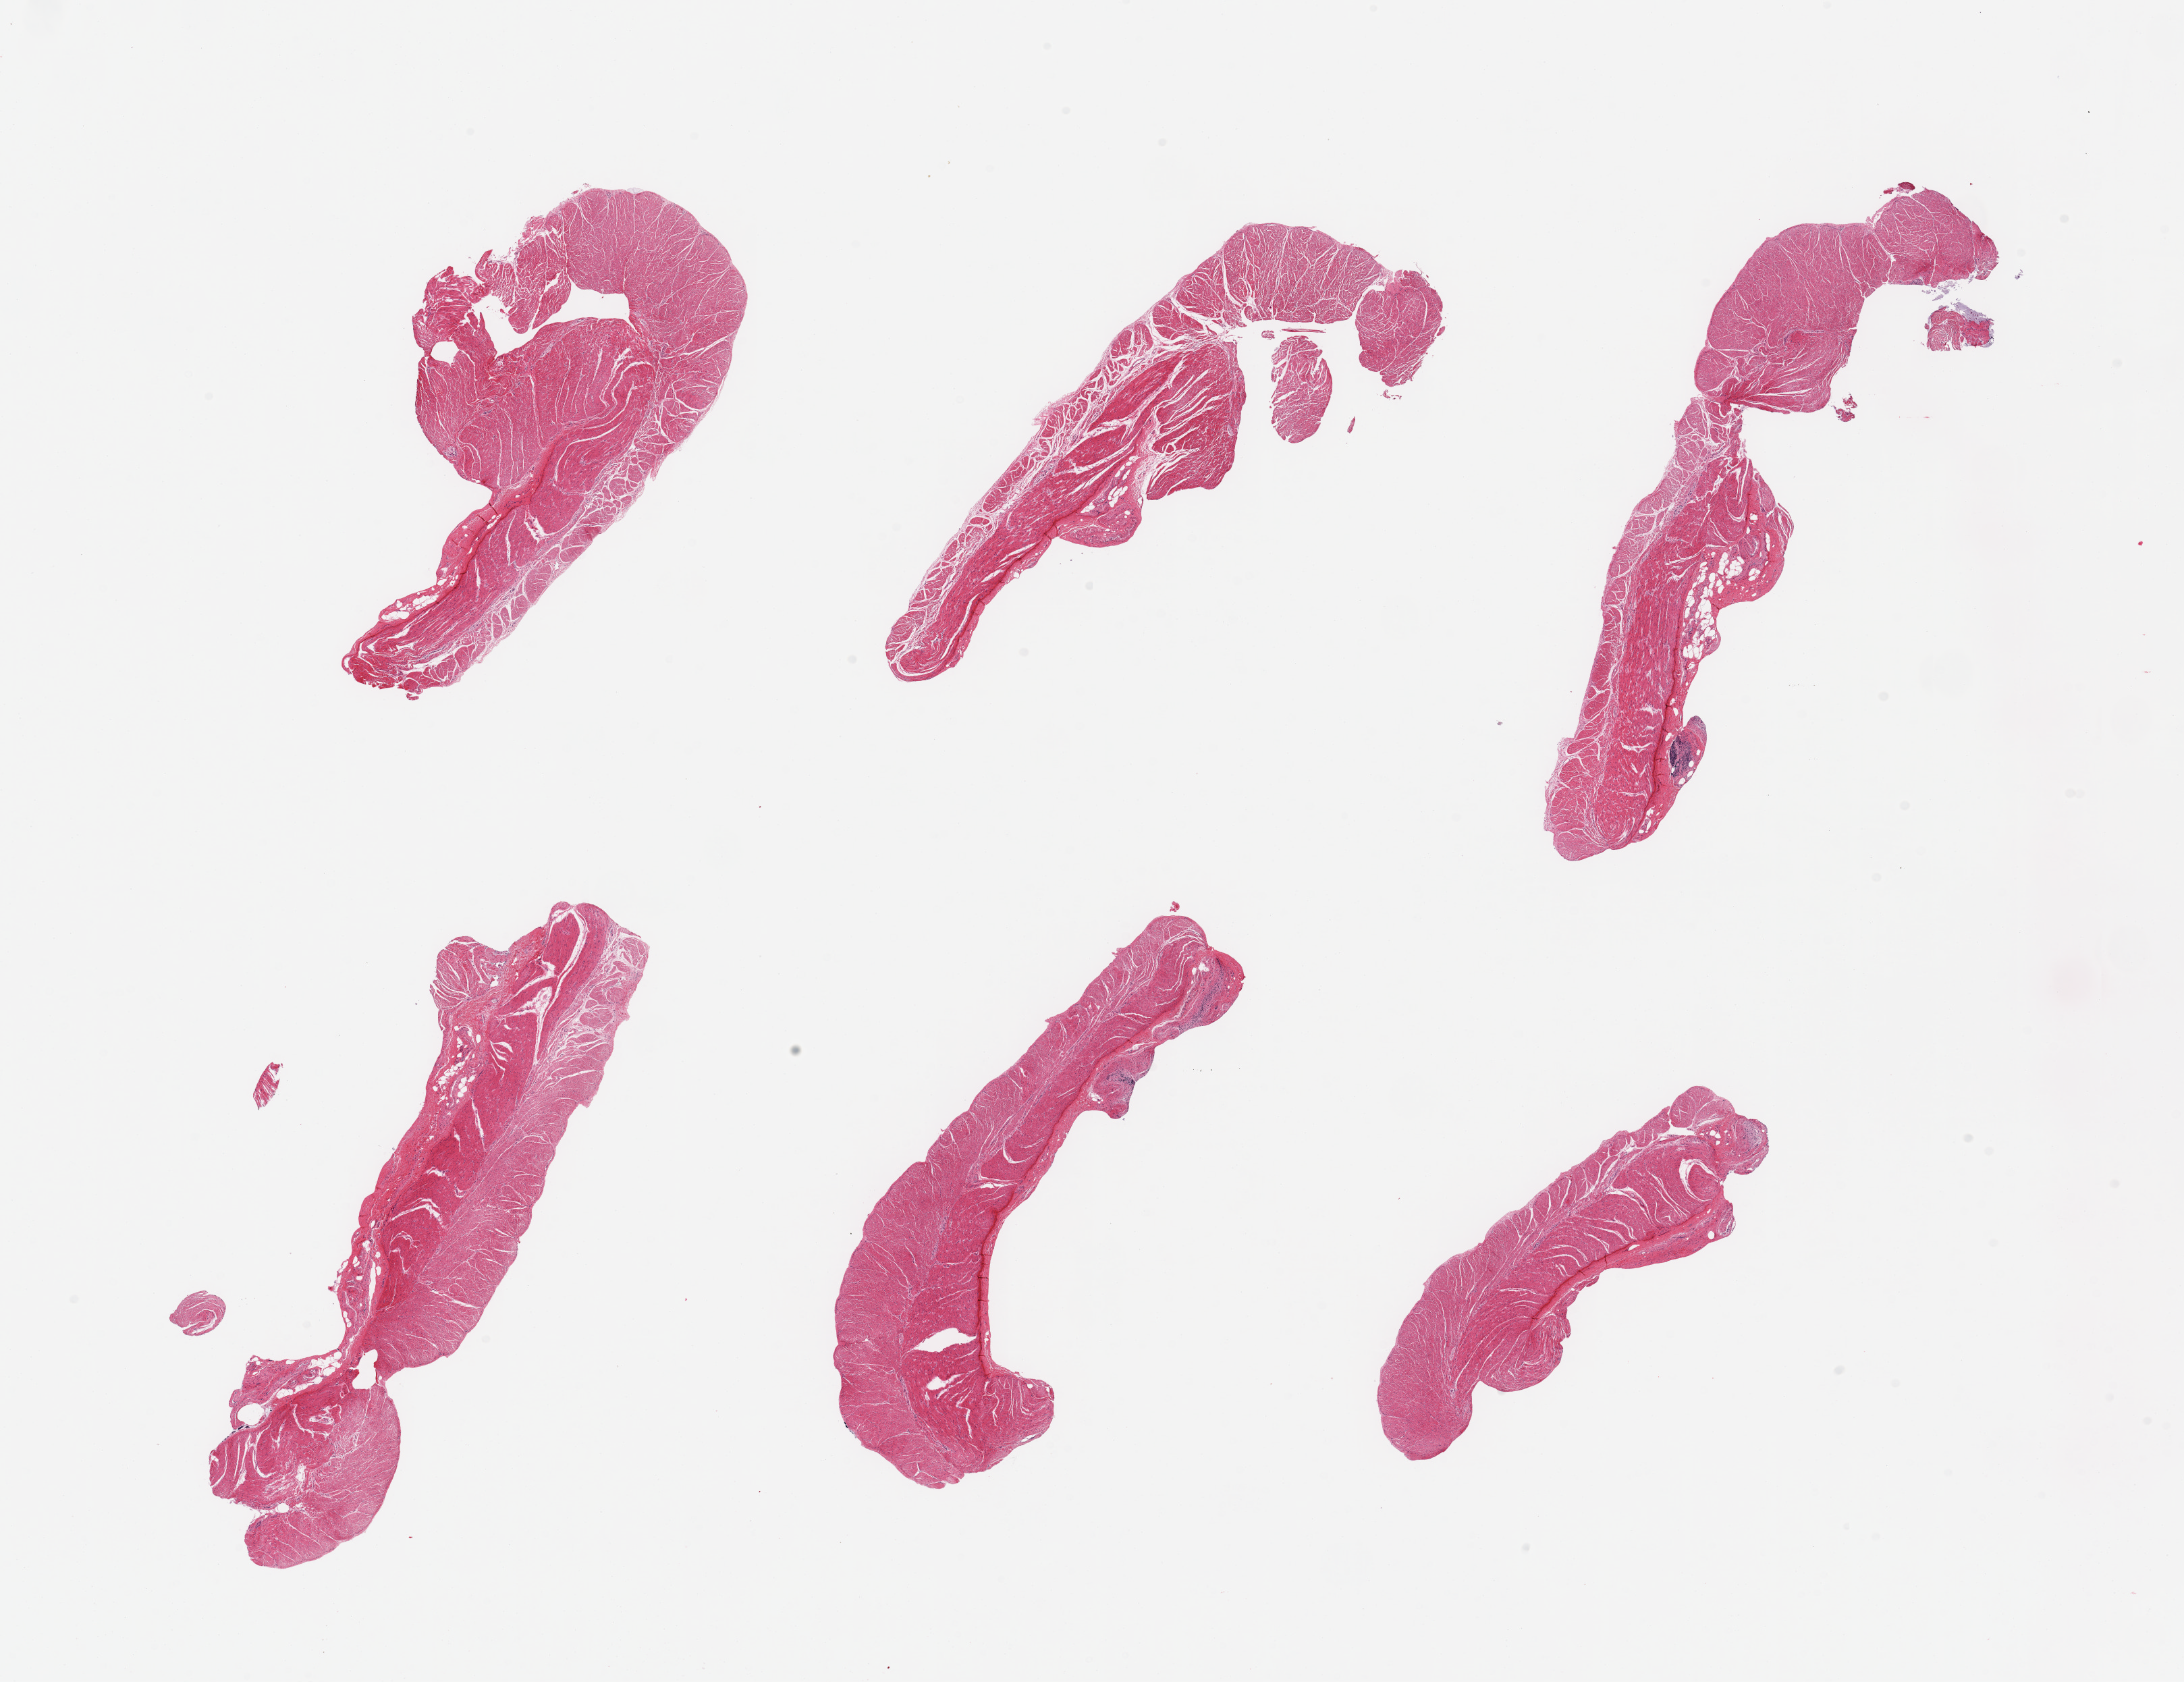
Digitized hematoxylin and eosin (H&E)-stained section, brightfield — shown as a low-resolution overview of the whole scanned area (about 25.6 x 19.7 mm). PAXgene-fixed paraffin-embedded (PFPE) section. Sampled site (target tissue): sigmoid colon. Tissue donor sample. Donor sex: male.
Review note (as recorded): 6 pieces, confirmed target muscularis.